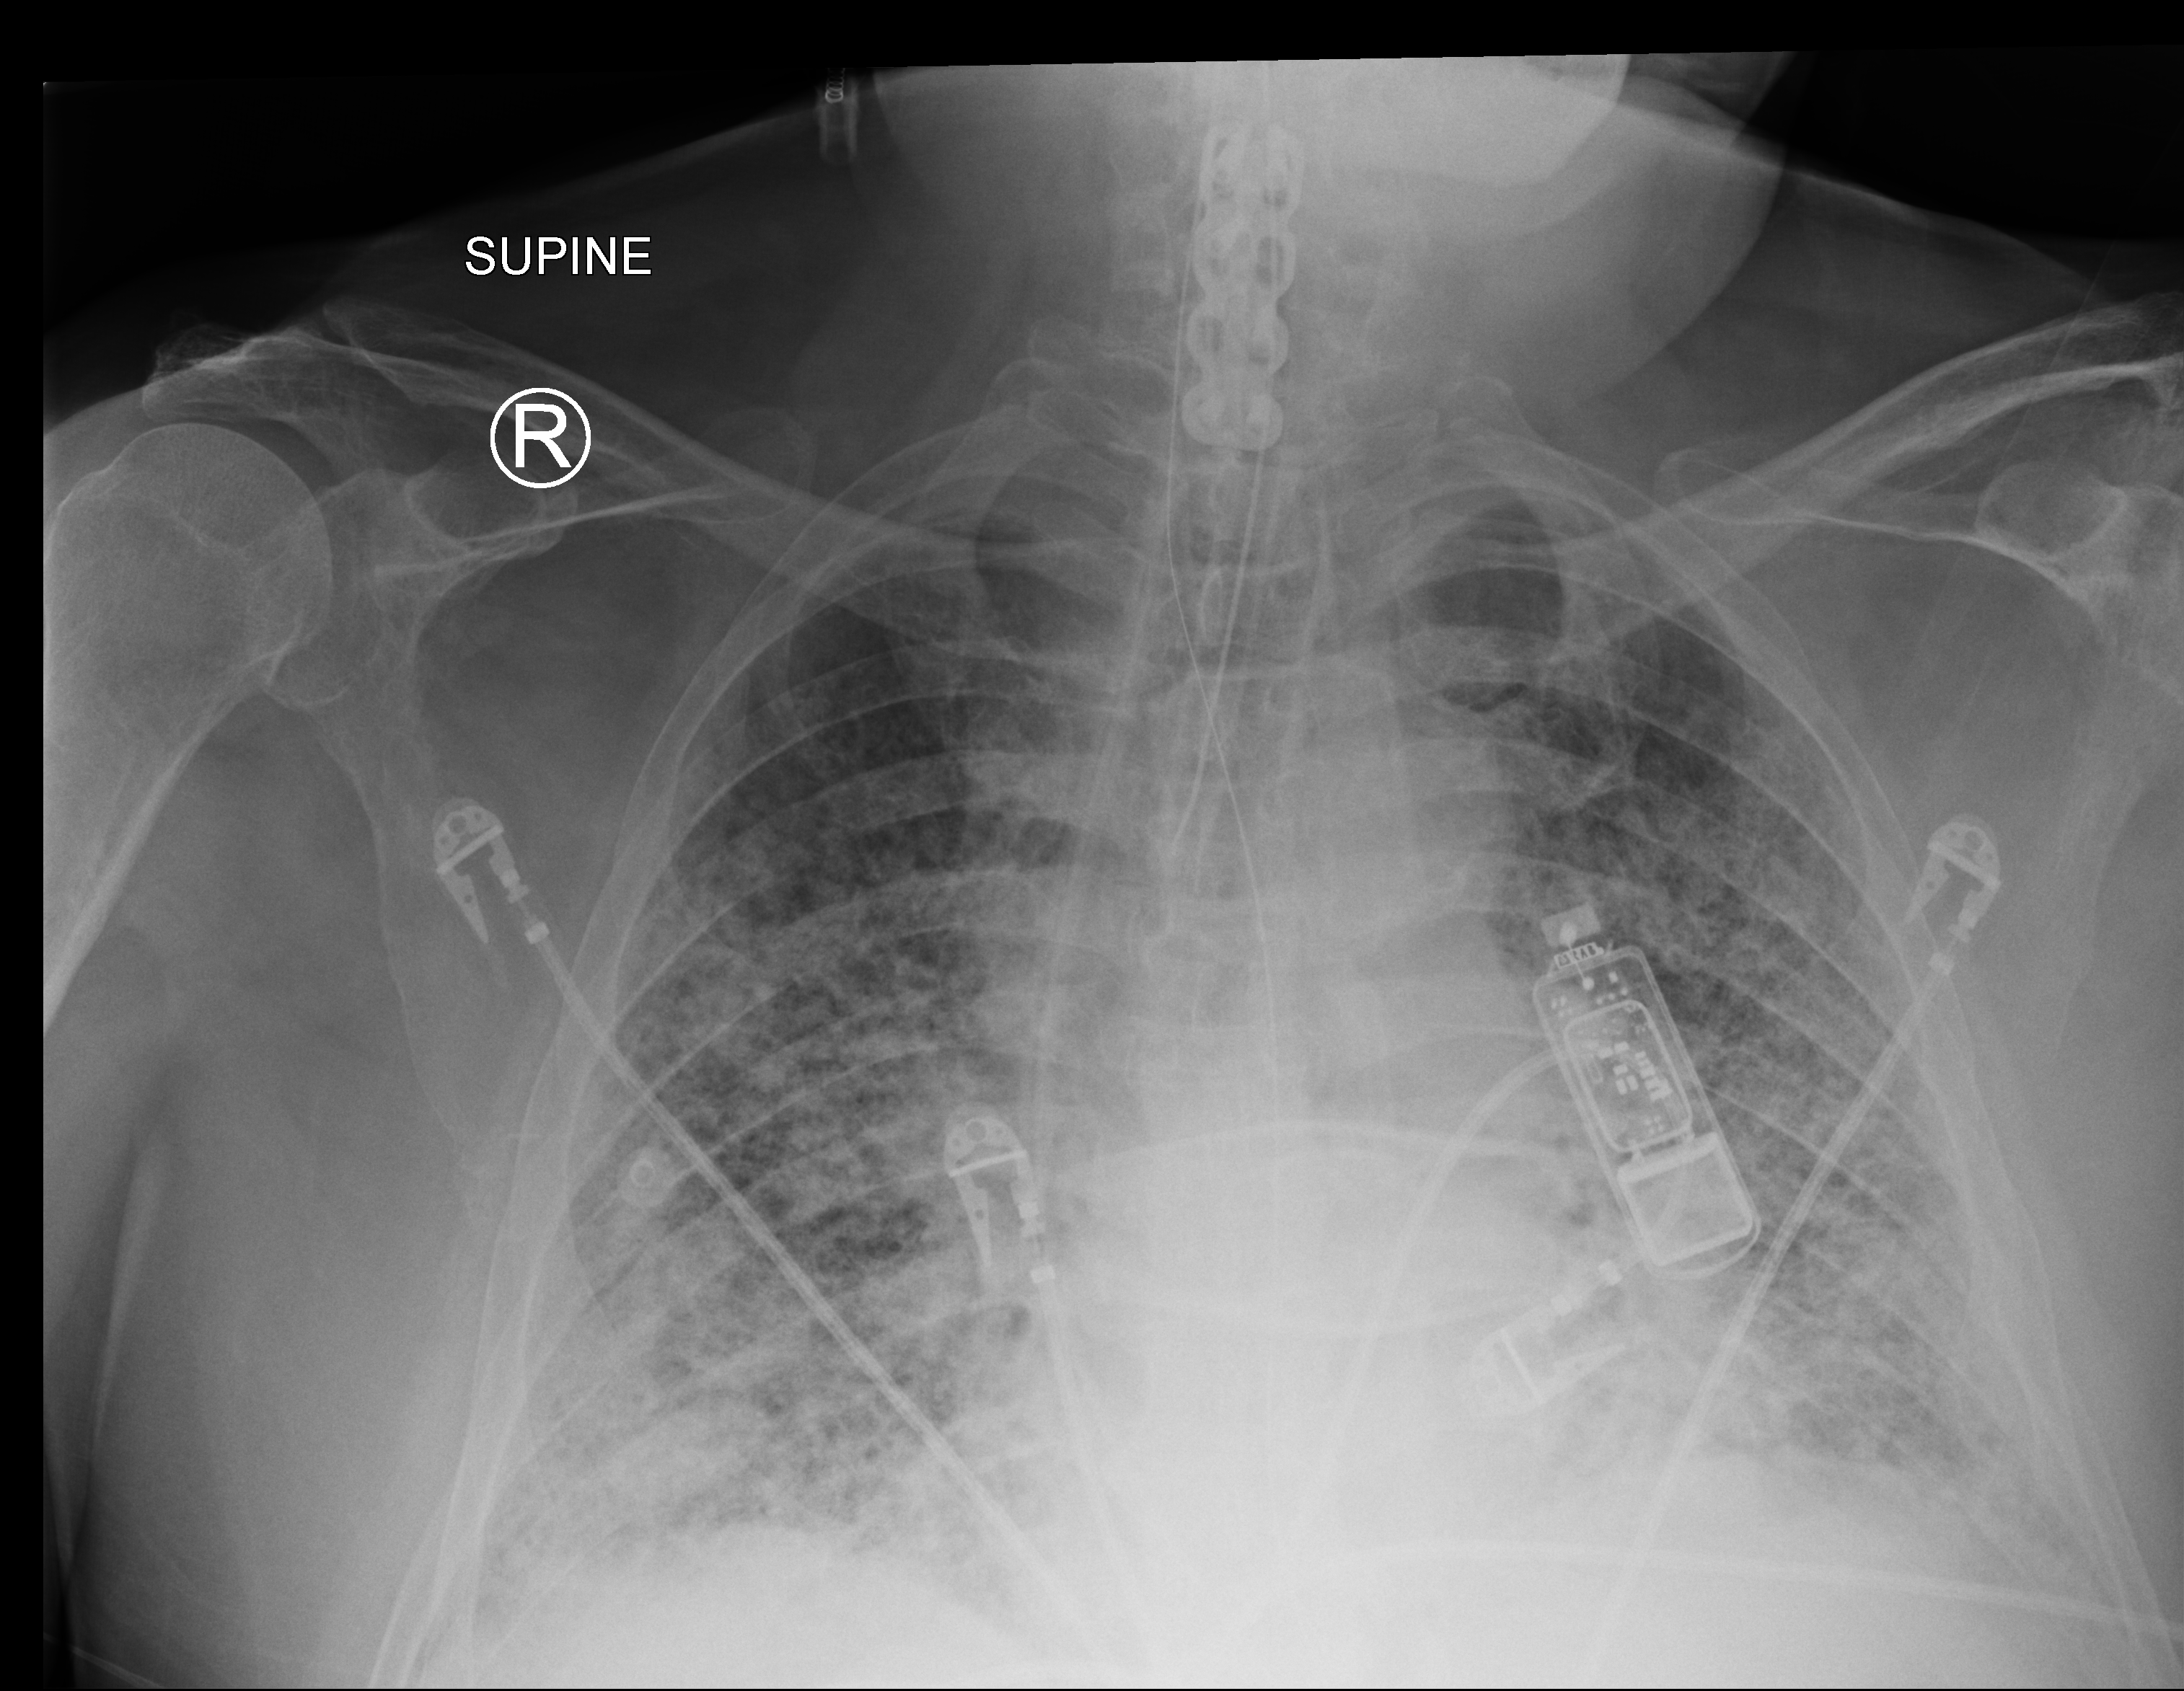
Bedside chest radiograph (computed radiography), anteroposterior (AP) projection. Male patient hospitalised with COVID-19, age 60–74 years.
Hospital-stay facts (about this admission, not read from this image; timing relative to this image not recorded): admitted to intensive care during this hospital stay: yes; chronic kidney disease (admission record): yes.